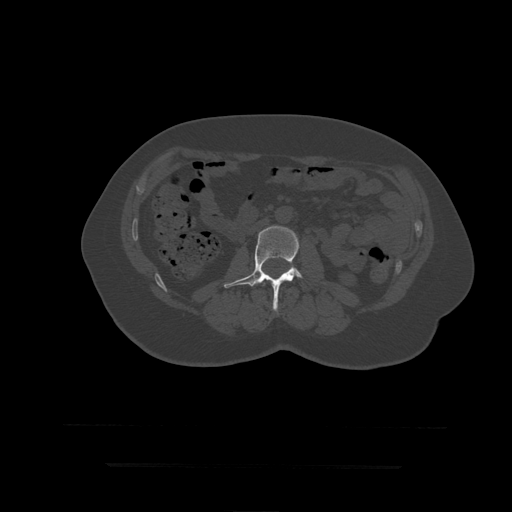
CT including the spine, one axial slice. Slice 125 of 399 in the series (ordered by position). 120 kVp. Bone window (W 1800 / L 400 HU). 1.25 mm slice thickness. 512 × 512 image matrix. Patient age 41 years. From the clinical record (not read from this slice): primary cancer: breast.
Structures marked on this image (semi-automatic segmentation, software-assisted and operator-edited):
- L2 vertebra: bounding box <262,282,265,286> (left, top, right, bottom; pixels)
- L3 vertebra: <224,226,303,312>